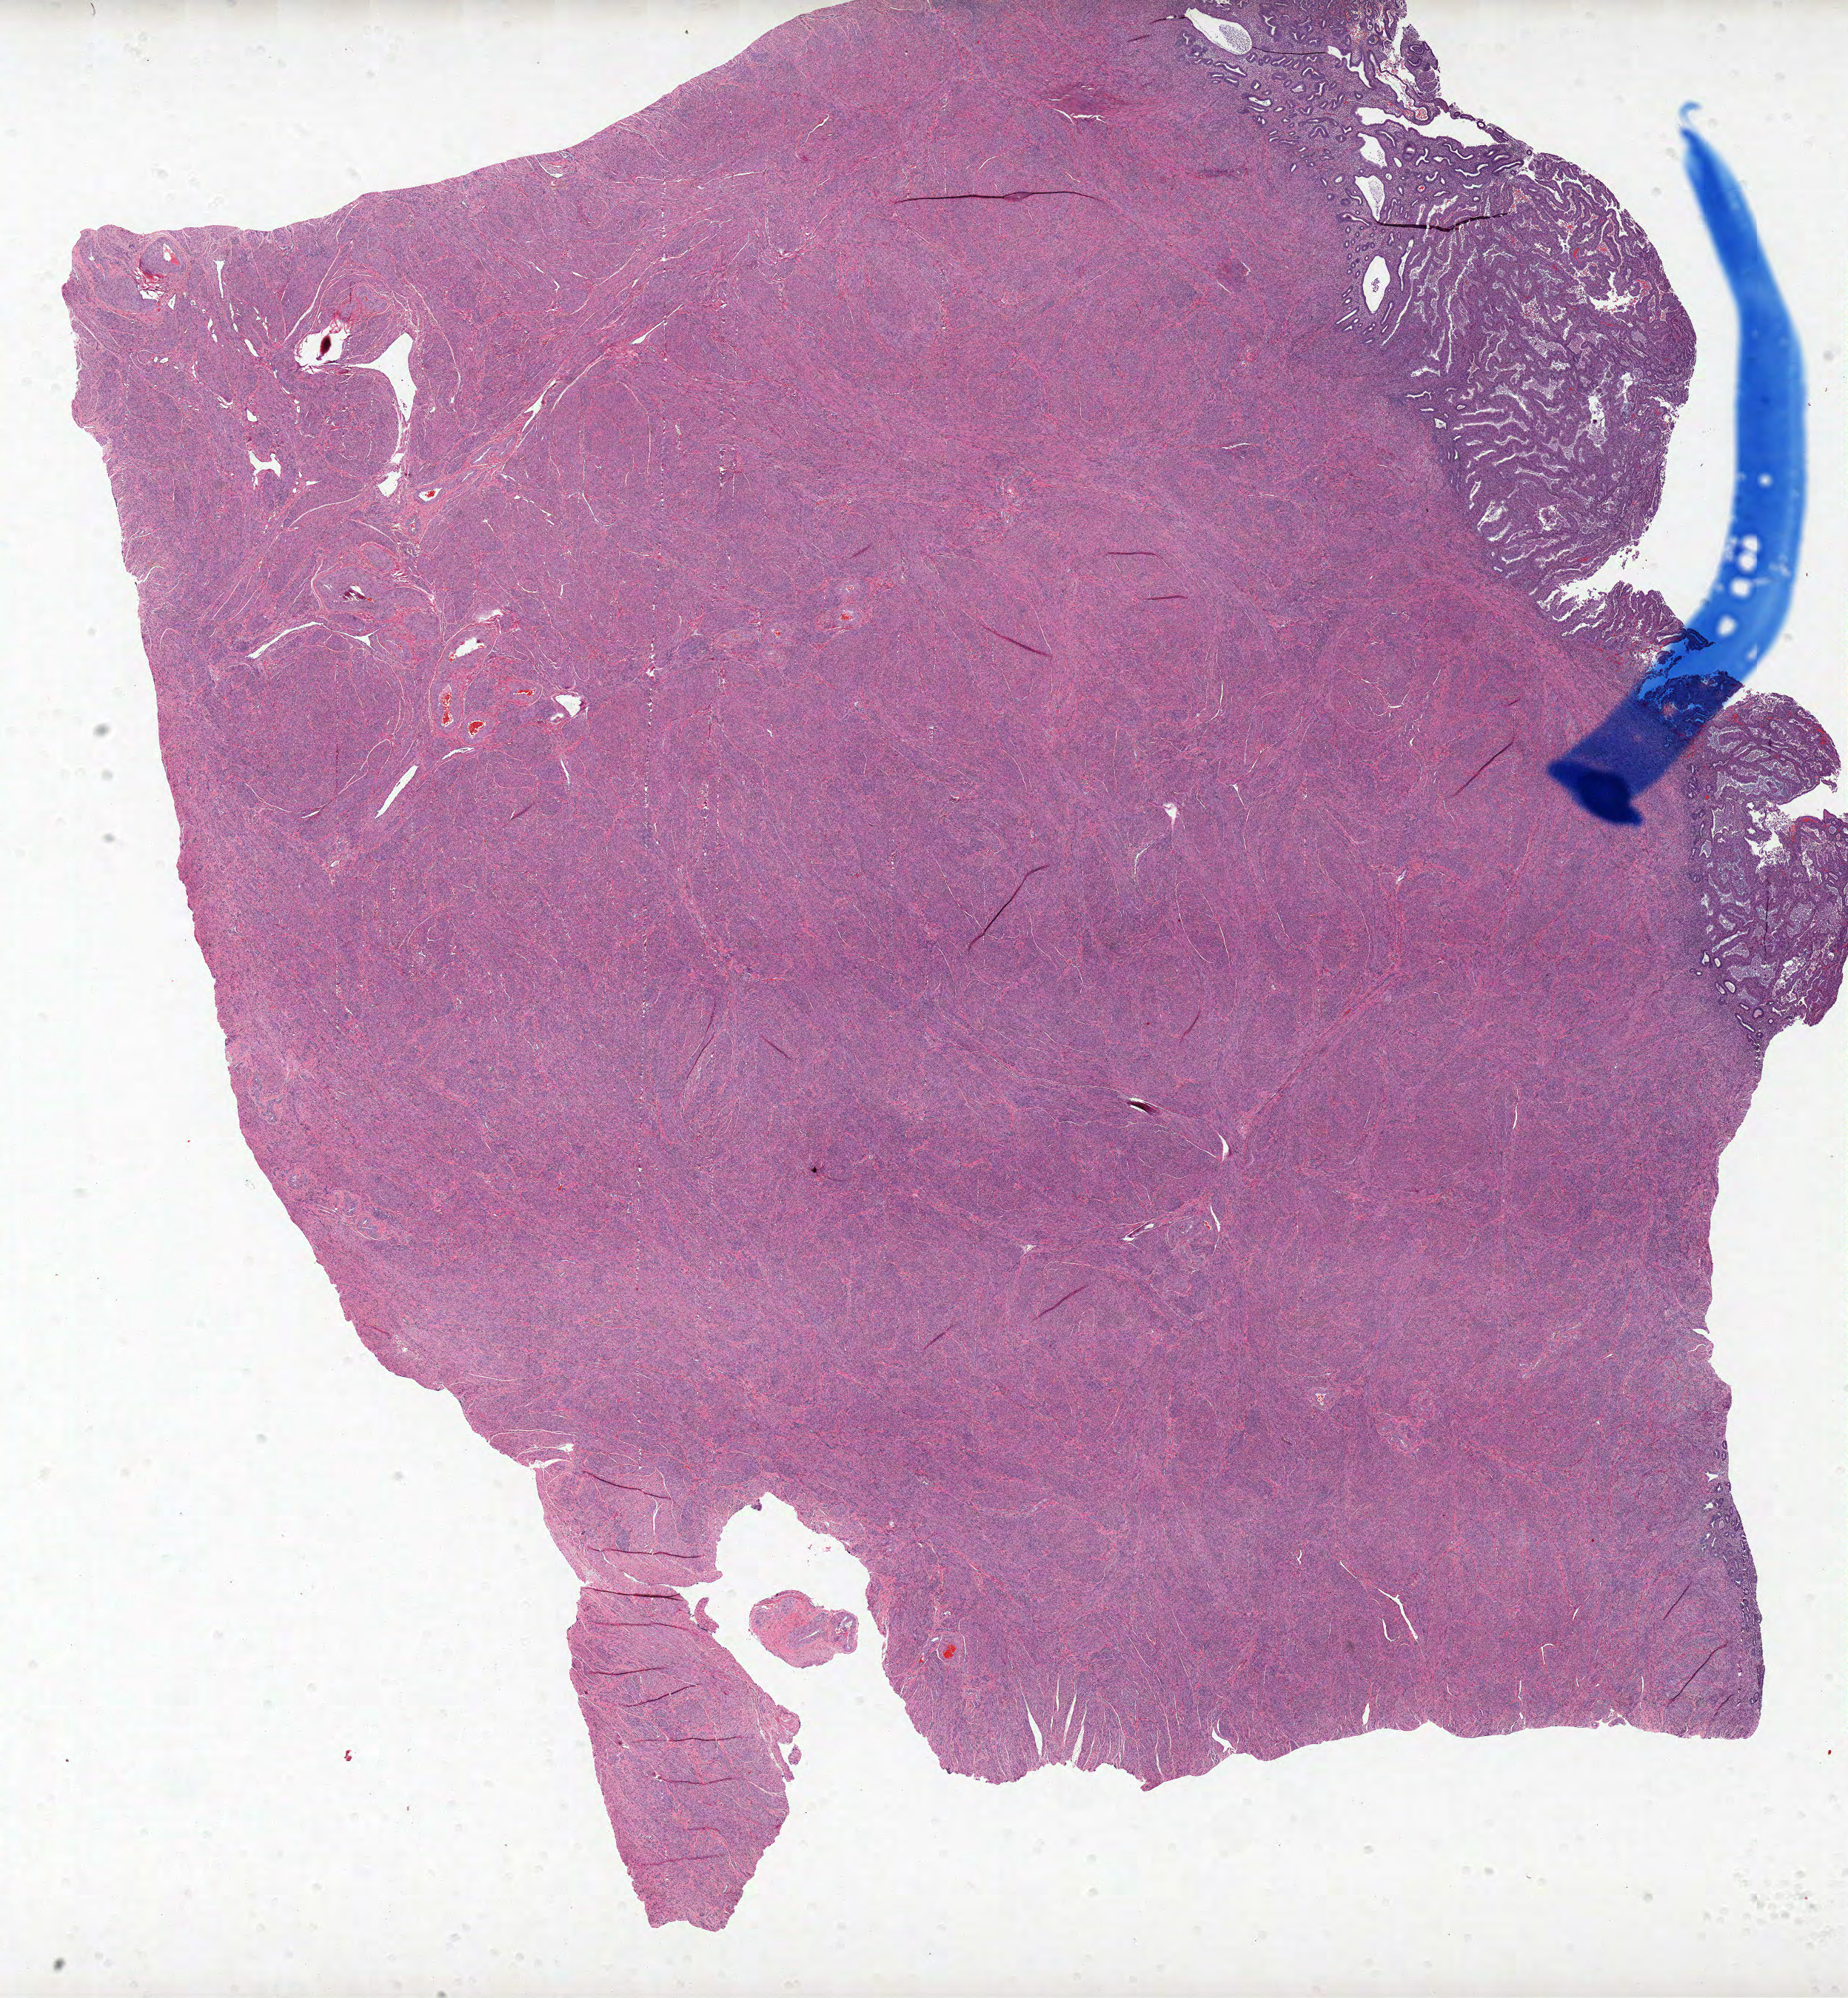
Whole-slide histology image, H&E-stained, low-resolution overview of the scanned area, about 19.9 x 21.5 mm (acquisition: 20x scan), formalin-fixed paraffin-embedded (FFPE) diagnostic section, sample: primary tumour, uterus. Patient: female, age at initial diagnosis 54 years. Histologic grade: G1 (well differentiated).
• diagnosis: Endometrioid adenocarcinoma, NOS (endometrium)
• FIGO stage: IA